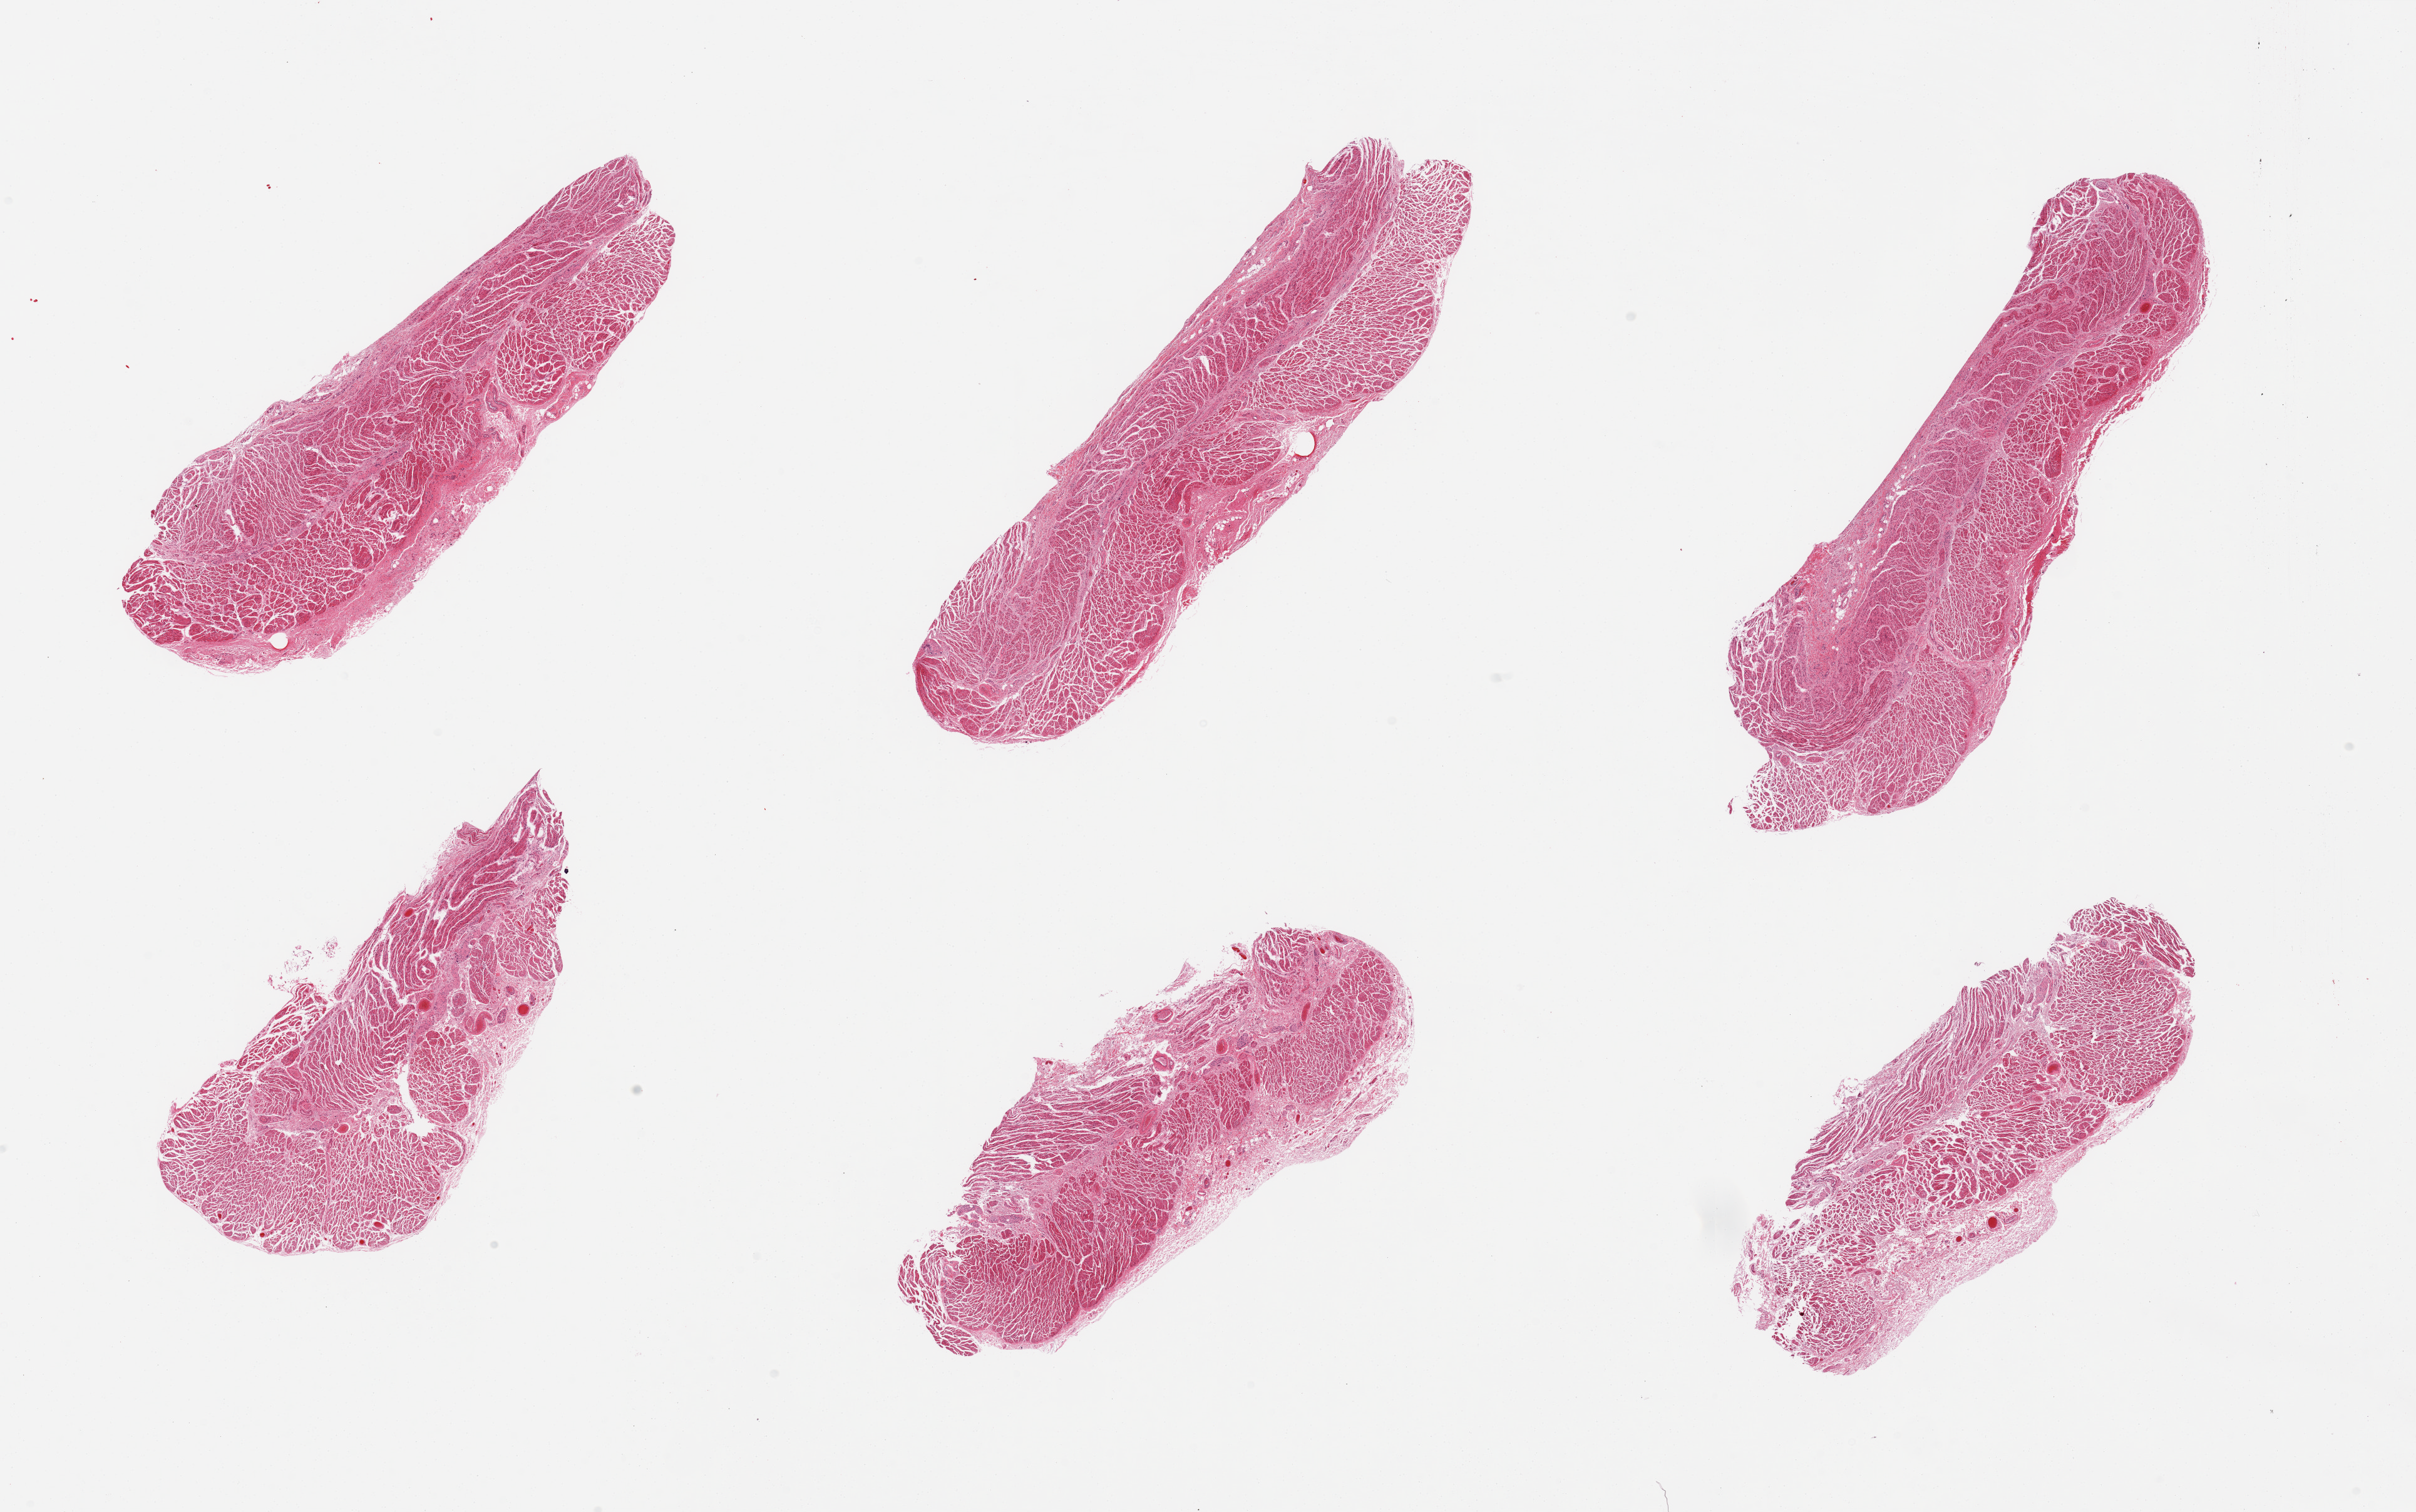
Digitized hematoxylin and eosin (H&E)-stained section, brightfield — a low-resolution overview of the entire scanned area, about 30.5 x 19.1 mm; PAXgene-fixed paraffin-embedded (PFPE) section; sampled site (target tissue): gastroesophageal junction; donor tissue sample. Donor: female.
* review note (as recorded): 6 pieces; well dissected muscle